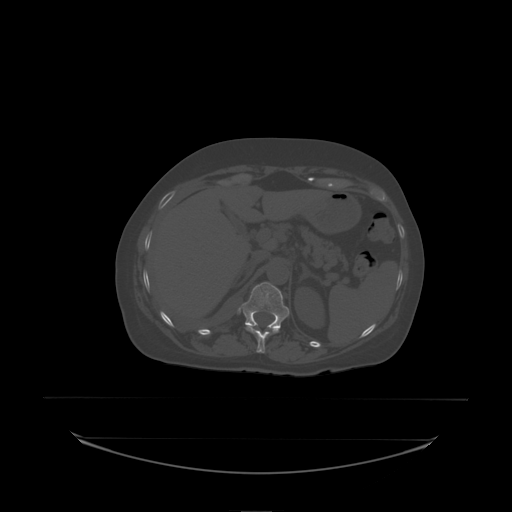
CT including the spine, one axial slice; slice 98 of 242 in the series (ordered by position); bone window (W 1800 / L 400 HU); 2.5 mm slice thickness; 512 × 512 image matrix, field of view 500 × 500 mm. Patient: female, 53 years. From the clinical record (not read from this slice): primary cancer: lung; vertebrae with lytic lesions (as recorded): T7, L1.
Outlined on this slice (semi-automatic segmentation, software-assisted and operator-edited):
- T11 vertebra: bounding box [x1, y1, x2, y2] px = [246, 326, 279, 338]
- T12 vertebra: [241, 283, 290, 331]